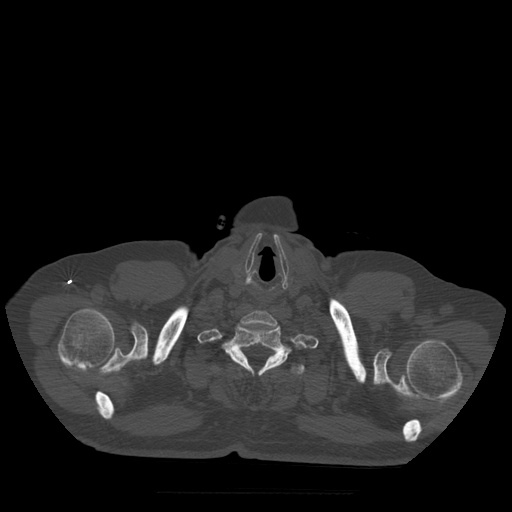
CT including the spine, one axial slice; slice 439 of 522 in the series (ordered by position); bone window (W 1800 / L 400 HU); 1.25 mm slice thickness; 512 × 512 image matrix. Patient age 72 years. Case-level facts recorded for this patient, not image findings: primary cancer: prostate.
Structures marked on this image (semi-automatic segmentation, software-assisted and operator-edited):
- T1 vertebra: bounding box <214,327,300,376> (left, top, right, bottom; pixels)
- T2 vertebra: <211,364,305,376>